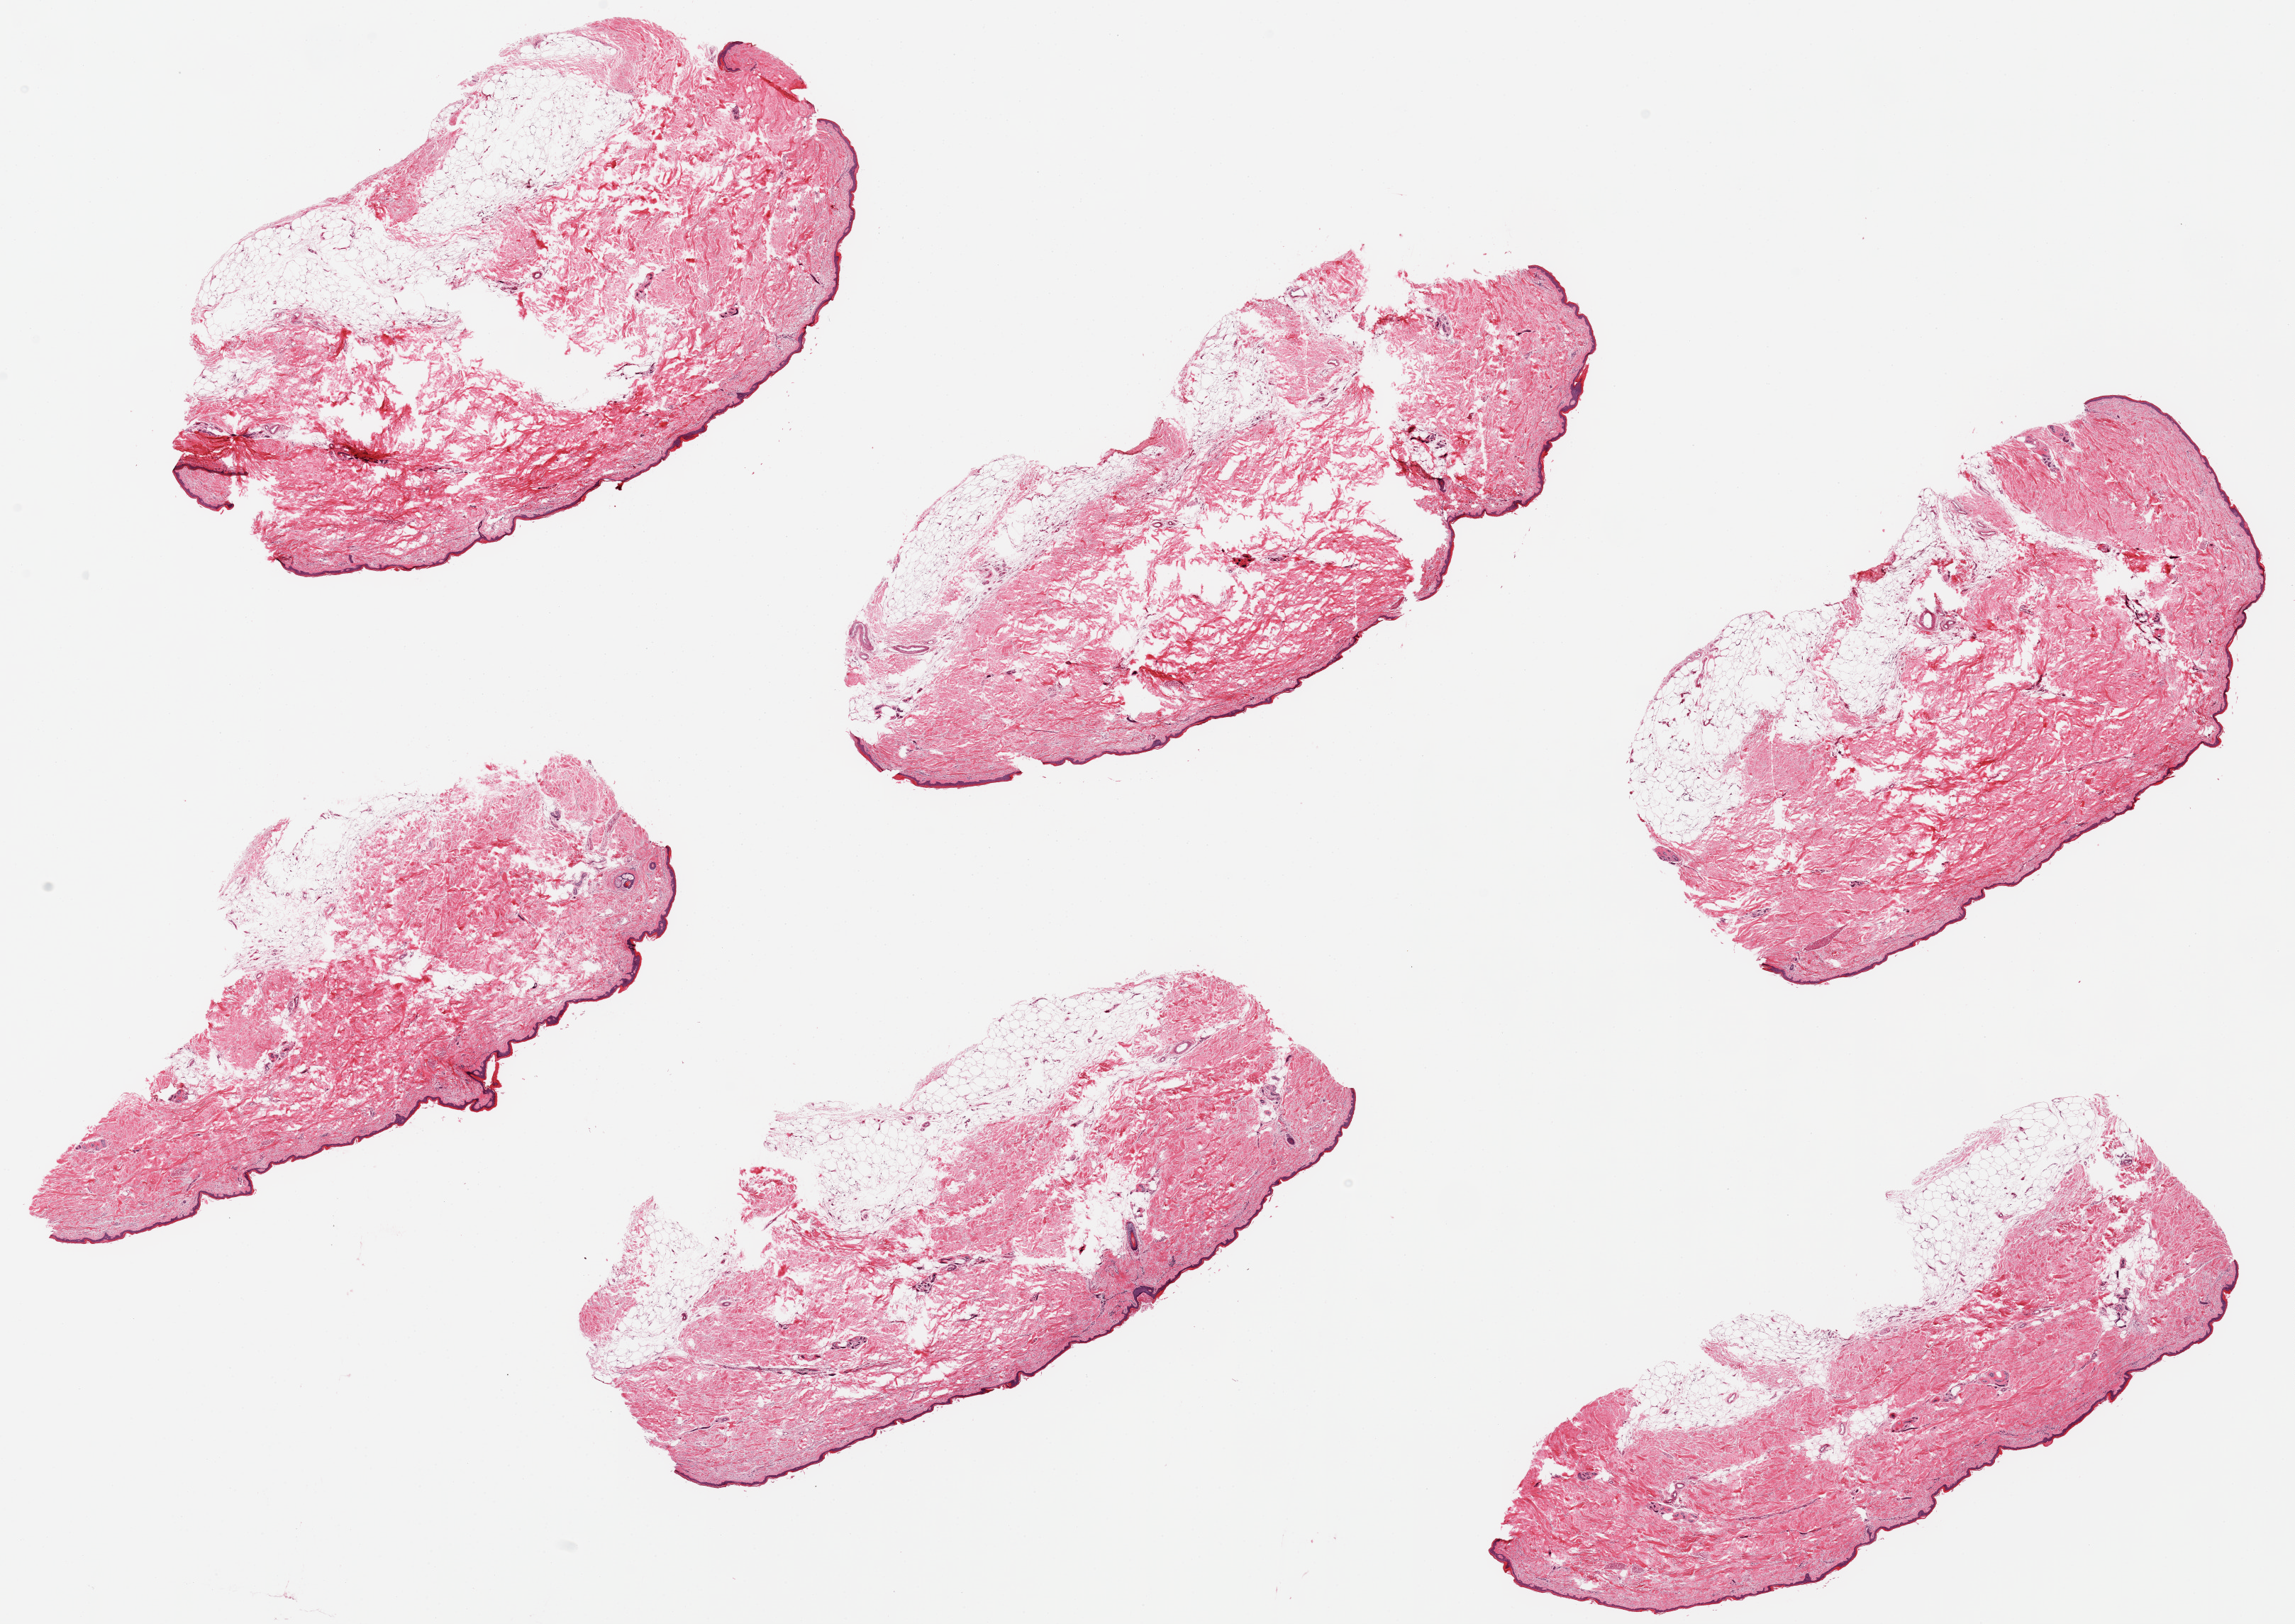
Whole-slide image, H&E stain, brightfield — low-resolution overview of the scanned area, about 25.6 x 18.1 mm. PAXgene-fixed paraffin-embedded (PFPE) section. Section of skin of lower leg (target tissue). Tissue donor sample.
Review note (as recorded): 6 pieces; all have up to 1 mm subcutaneous fat.